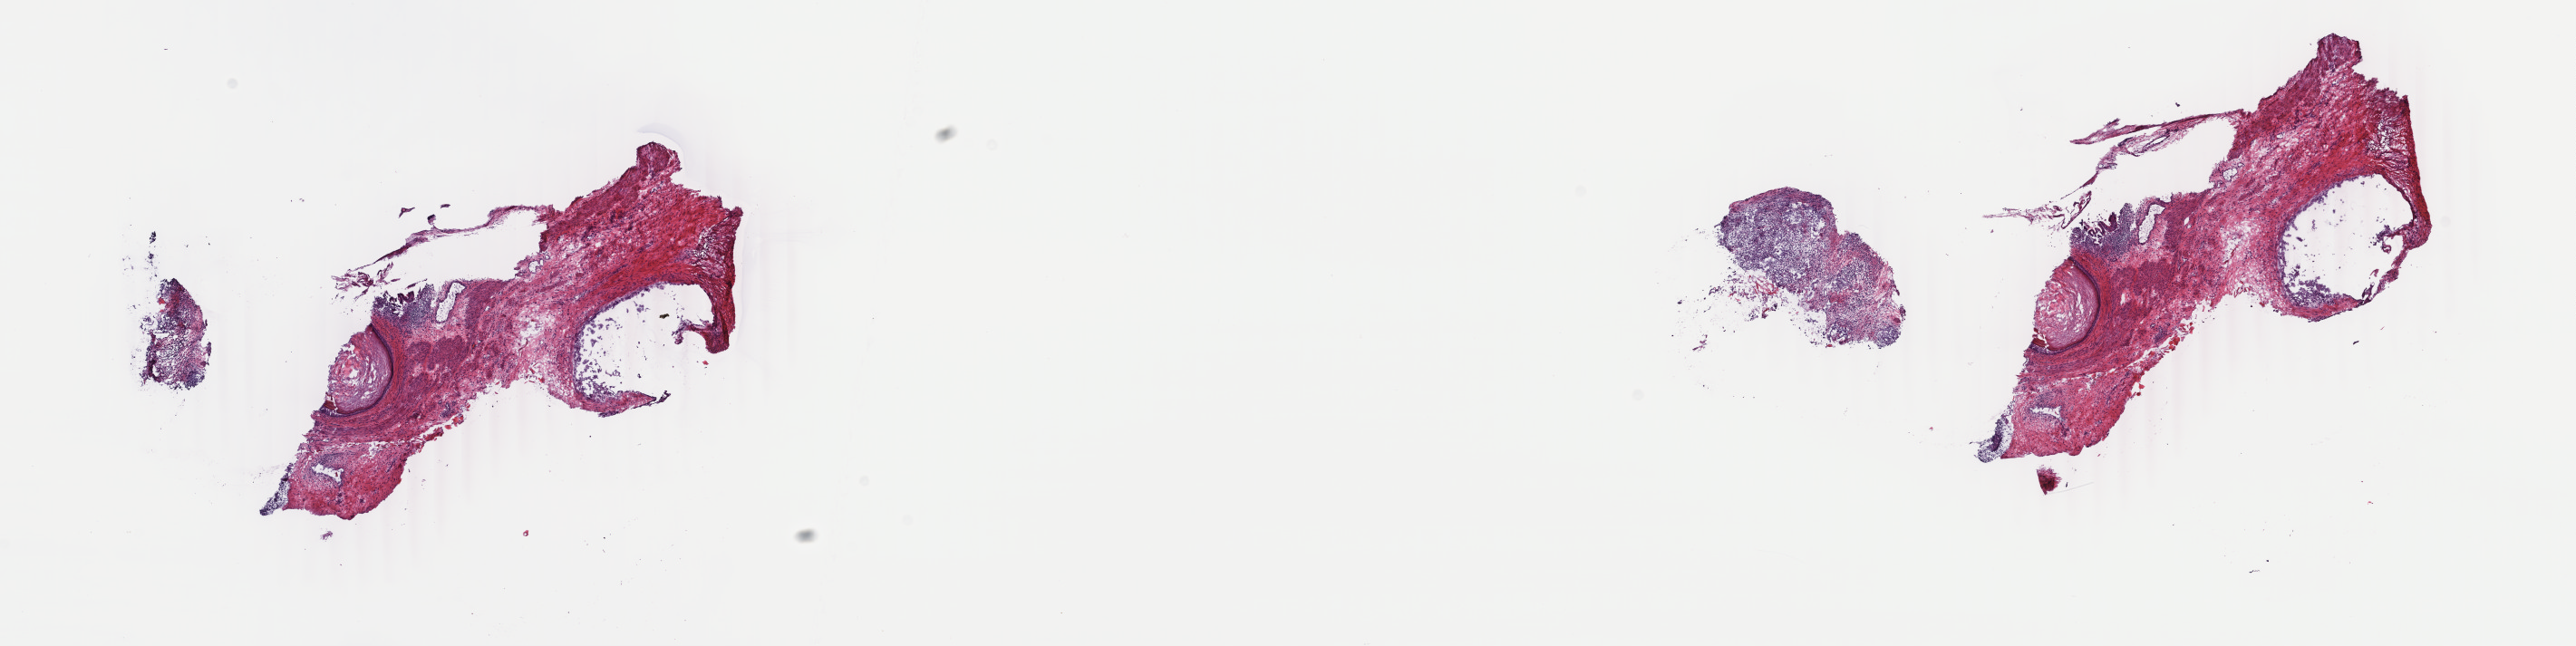
Digitized H&E tissue section (whole slide), whole scanned area (about 22.6 x 5.7 mm, slide scanned at 40x) shown as a low-resolution overview; frozen section; testis, primary tumour sample. Male, age 24 years at initial diagnosis. Slide review estimates, as recorded: tumour cells 70%, tumour nuclei 70%, normal cells 0%, stromal cells 30%, necrosis 0%. Infiltration values recorded for this section: lymphocyte infiltration 2%, monocyte infiltration 1%, neutrophil infiltration 1%.
AJCC pathologic stage: IS. Diagnosis: Teratoma, benign. Laterality: left.